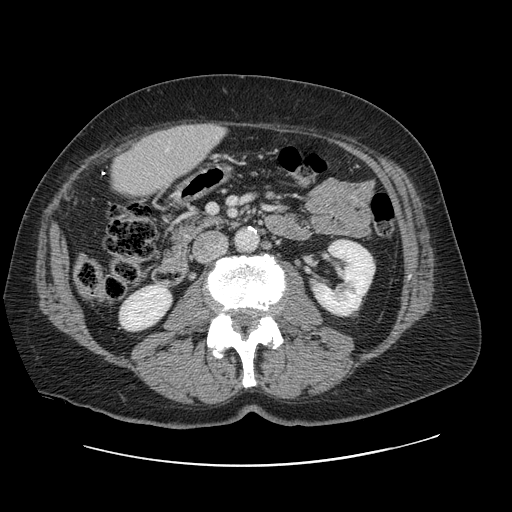
Contrast-enhanced abdominal CT, one axial slice. Slice 21 of 138 in the series (ordered by position). 120 kVp. Soft-tissue window (W 400 / L 40 HU). 512 × 512 image matrix, field of view 402 × 402 mm. Male patient, age 71 years. Case-level facts recorded for this patient, not image findings: diagnosis: colorectal cancer liver metastases, imaged before liver resection; multiple liver metastases: no; largest metastasis: 3.3 cm; chemotherapy before resection: no.
Annotated regions visible in this slice (manually delineated by an expert):
- liver: bounding box <113,124,224,197> (left, top, right, bottom; pixels)
- planned liver remnant (the part of the liver to remain after resection): <111,135,177,197>